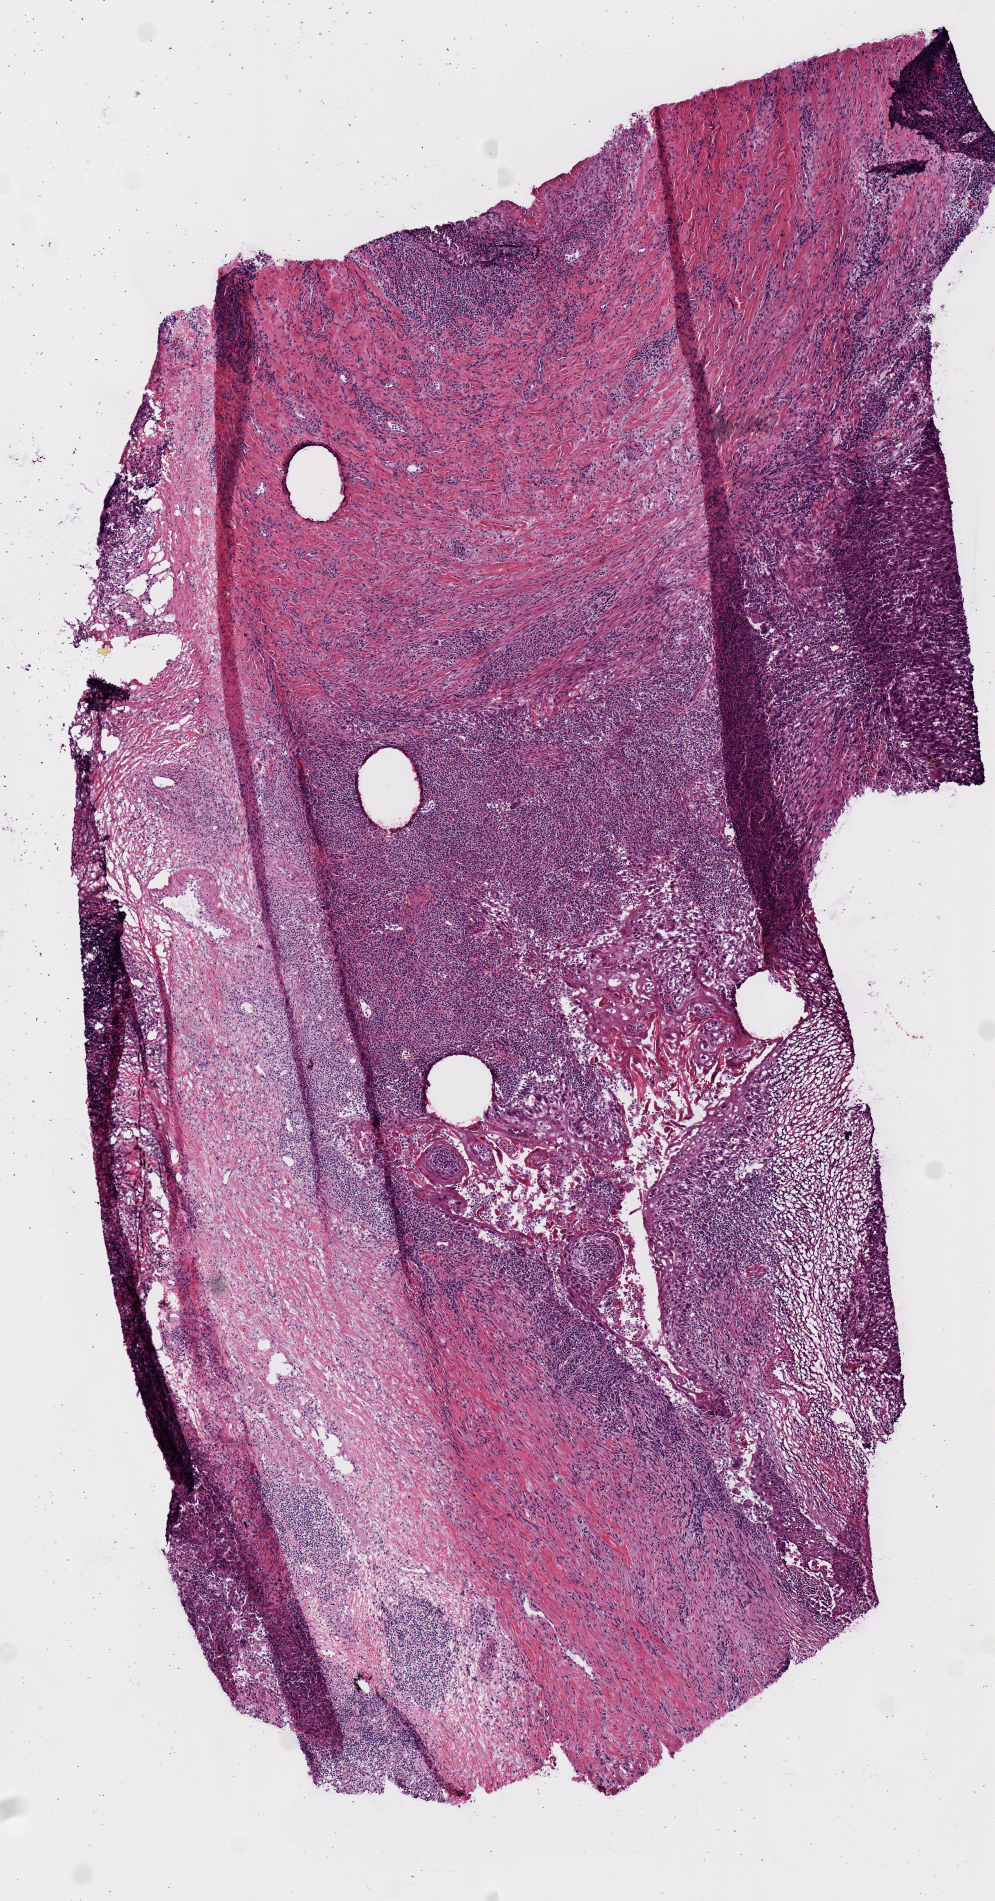
Whole-slide histology image, H&E-stained — a low-resolution overview of the entire scanned area, about 3.9 x 7.5 mm, frozen section from the top of the tissue portion, lung, primary tumour sample. Male patient; age at initial diagnosis 70 years. Slide review estimates, as recorded: tumour cells 90%, tumour nuclei 75%, normal cells 0%, stromal cells 10%, necrosis 0%.
AJCC pathologic stage: IB (6th edition). Diagnosis: Squamous cell carcinoma, NOS (upper lobe, lung).